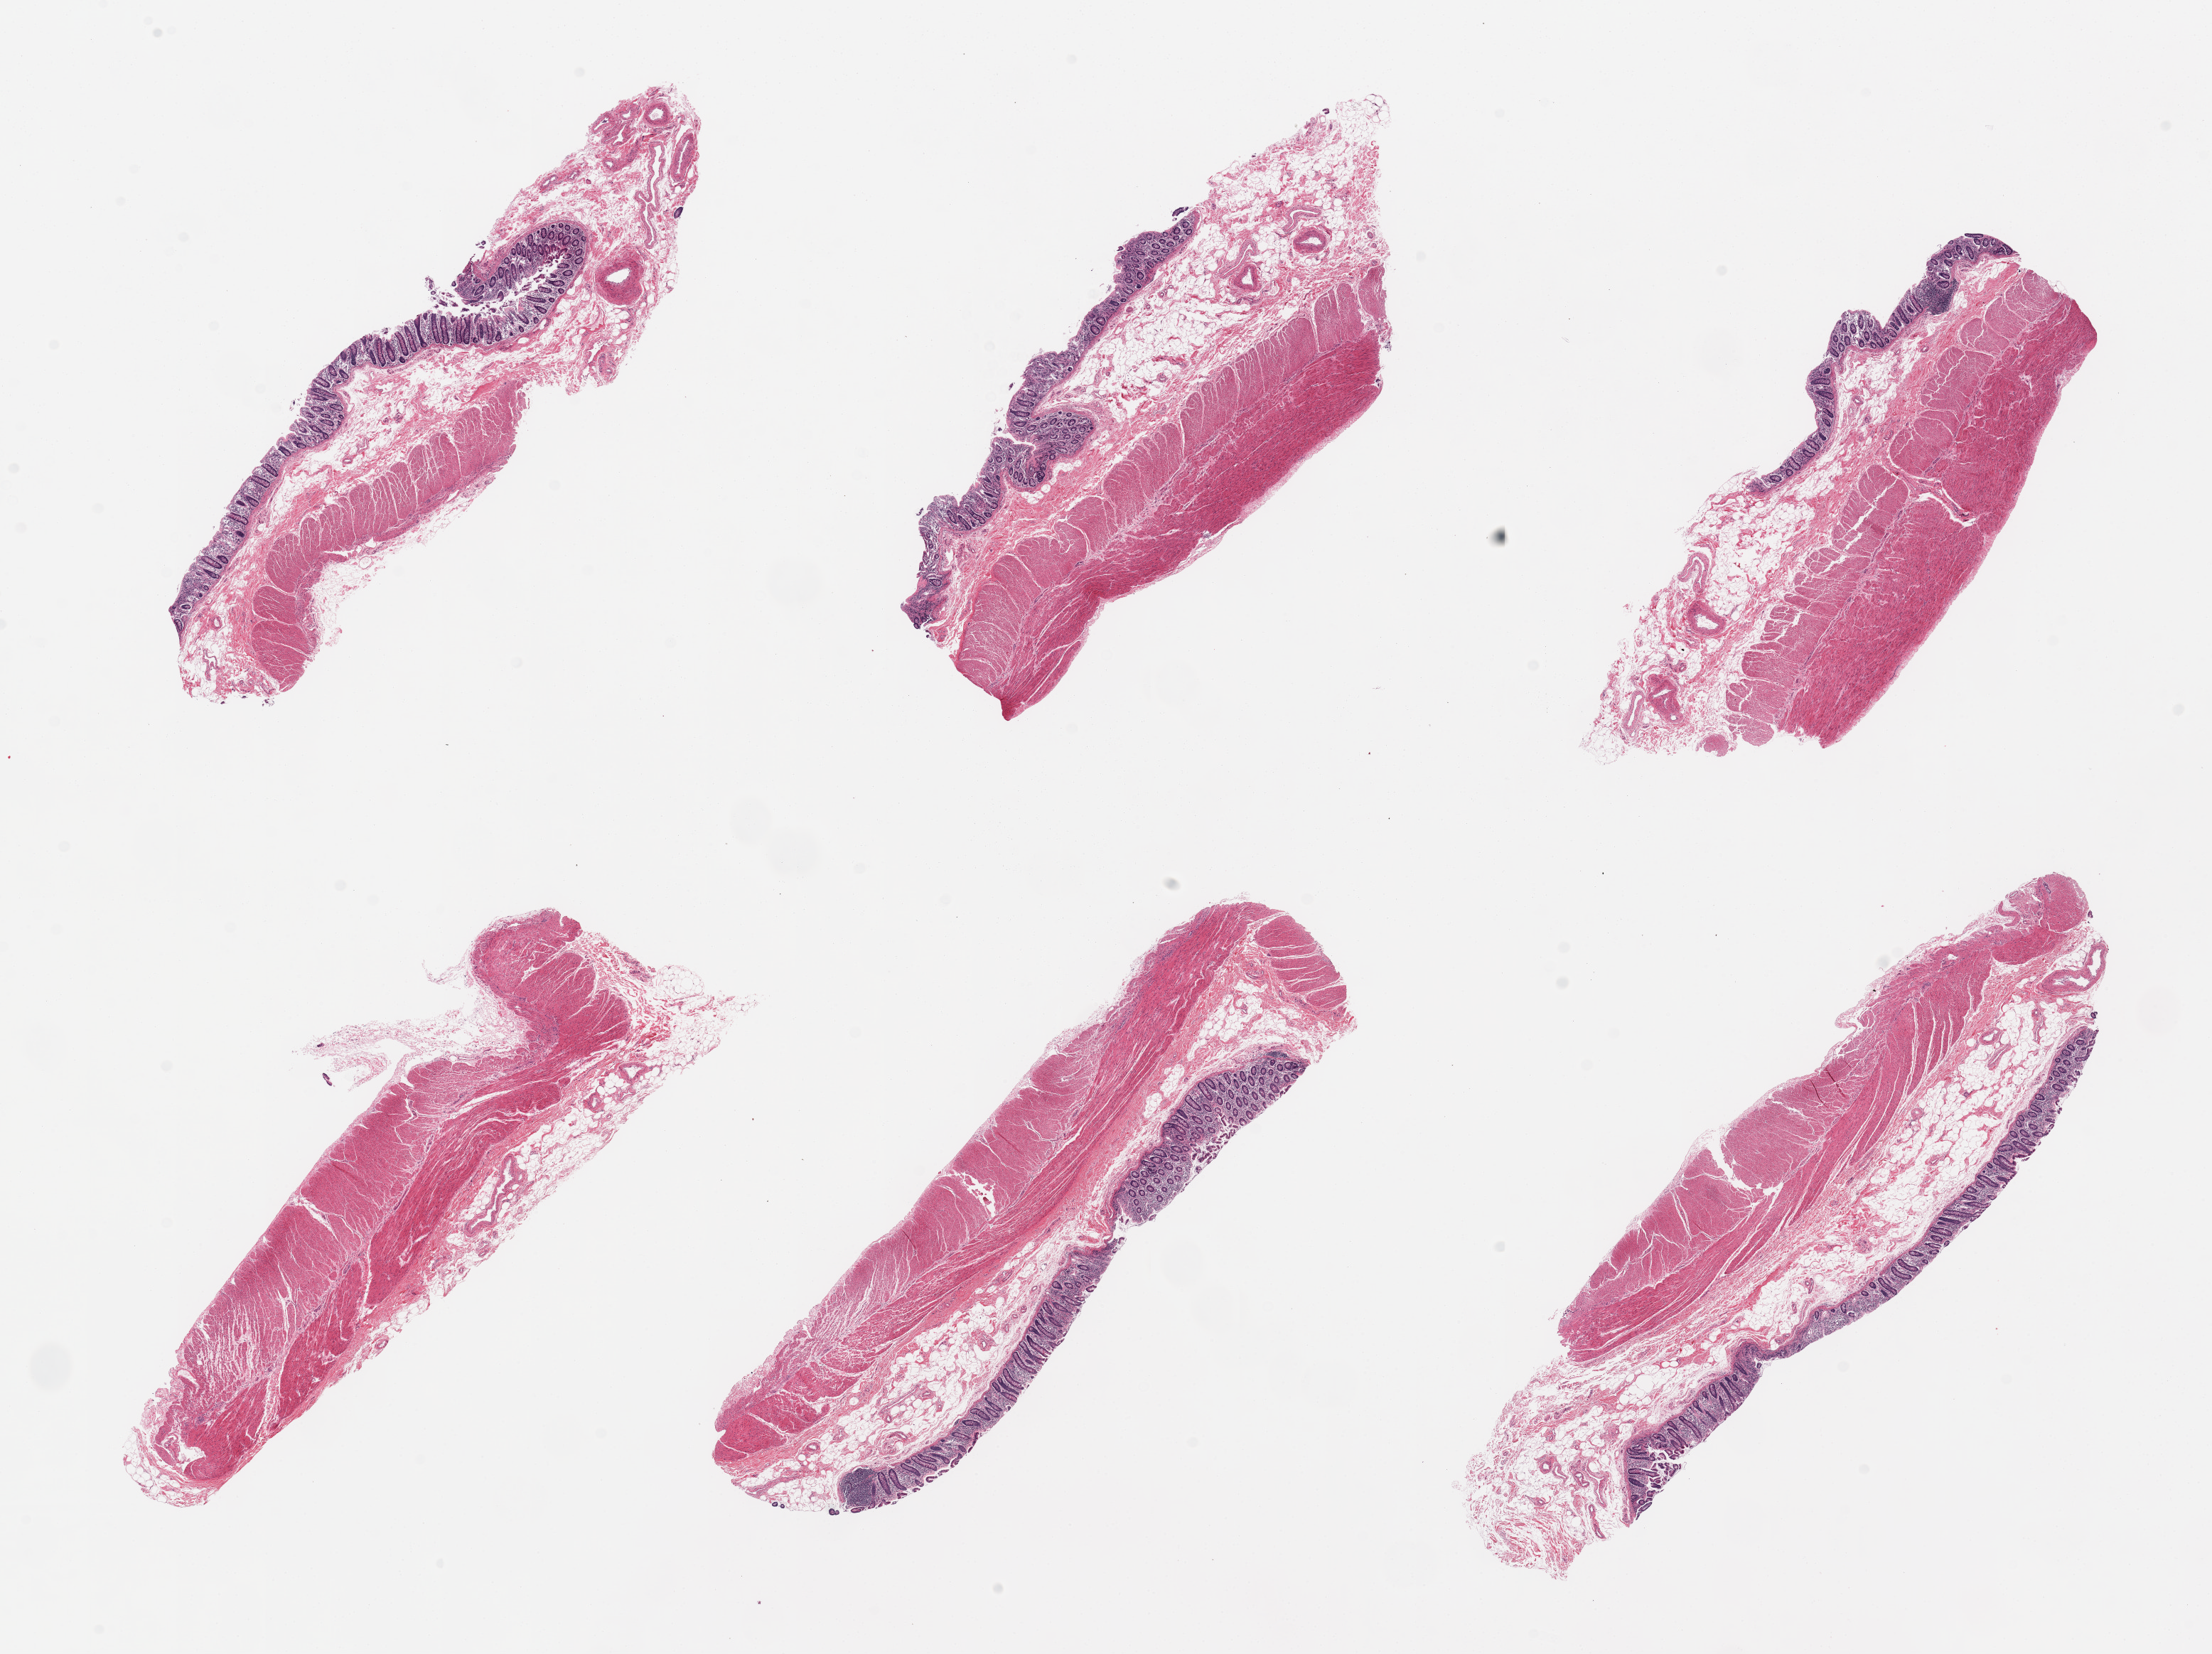
Whole-slide image, hematoxylin and eosin (H&E) stain, shown as a low-resolution overview of the whole scanned area (about 24.6 x 18.4 mm). PAXgene-fixed, paraffin-embedded tissue. Section of transverse colon (target tissue). Tissue donor sample. Donor: male.
Review note (as recorded): 6 pieces, mucosa ~0.4mm, ~20% thickness, not well preserved, missing in some sections.